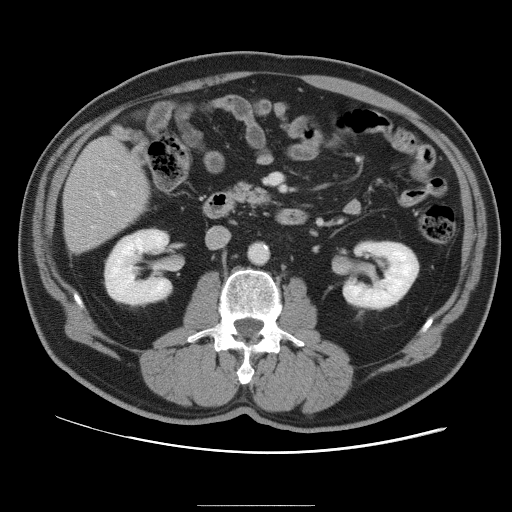
Contrast-enhanced abdominal CT, one axial slice; position 33 of 105 along the scan axis; intravenous contrast given; soft-tissue window (W 400 / L 40 HU); 512 × 512 image matrix, field of view 399 × 399 mm. Male patient, age 64 years. From the clinical record (not read from this slice): diagnosis: colorectal cancer liver metastases, imaged before liver resection; multiple liver metastases: yes; largest metastasis: 3 cm; disease in both lobes: yes.
Annotated regions visible in this slice (manually delineated by an expert):
- hepatic veins: bounding box <92,191,115,228> (left, top, right, bottom; pixels)
- liver: <64,139,147,252>
- planned liver remnant (the part of the liver to remain after resection): <64,139,149,234>
- portal vein (with intrahepatic branches): <95,192,99,197>